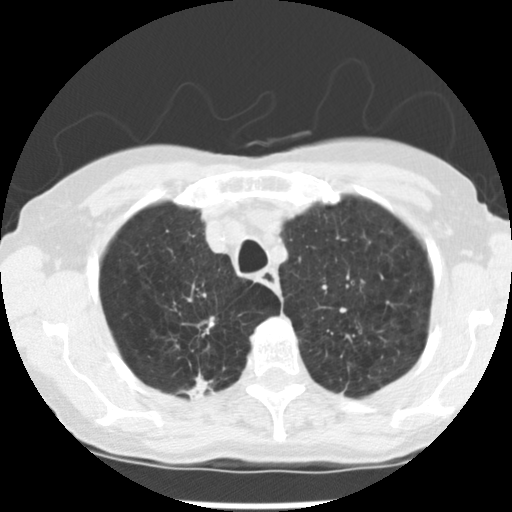
Chest CT (low-dose screening protocol), one axial image. First (baseline) screen. Lung window (W 1500 / L -600 HU). 2.5 mm slice thickness. Standard (soft-tissue) reconstruction kernel (STANDARD). 120 kVp. Slice 44 of 265 in the series. 512 × 512 image matrix, field of view 300 × 300 mm. Female participant, aged 72 years at enrolment.
- 2 expert-annotated lung lesions on this slice (largest first), bounding box [x1, y1, x2, y2] px = [182, 366, 230, 405]; [188, 309, 232, 345].
- The screening reader recorded 3 non-calcified nodules or masses ≥4 mm on this exam; which of them these boxes mark is not recorded.